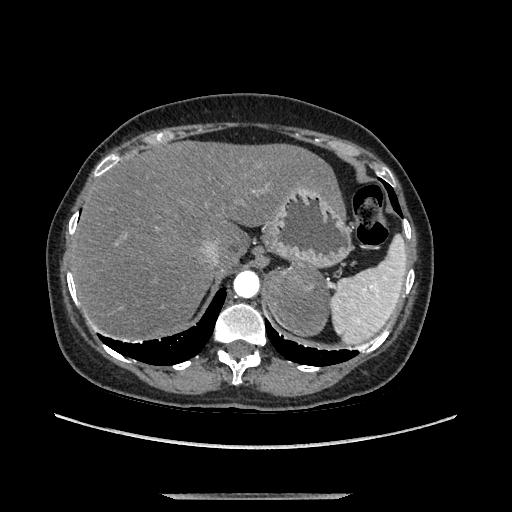
Contrast-enhanced abdominal CT, one axial slice; slice 106 of 169 in the series (ordered by position); soft-tissue window (W 400 / L 40 HU); 1.25 mm slice thickness; 512 × 512 image matrix. Female patient. From the clinical record (not read from this slice): diagnosis: adrenocortical carcinoma; tumour side: left adrenal; tumour size at pathology: 9 cm; Ki-67 index: 2 %; stage (as recorded): 3.
Outlined on this slice (semi-automatically segmented with operator editing):
- mass: bounding box [x1, y1, x2, y2] px = [269, 263, 327, 334]